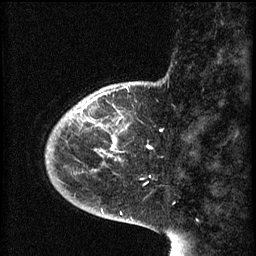
Breast MRI (dynamic contrast-enhanced), one sagittal slice; slice 12 of 60 in the series (ordered by position); 3 images stored at this slice position (order not interpretable as contrast timing); 1.5 T; TE 4.2 ms, TR 8.1 ms; 2 mm slice thickness; 256 × 256 image matrix, field of view 200 × 200 mm. Patient: female, 44 years.
Structures marked on this image (semi-automatic segmentation, software-assisted and operator-edited):
- analysis volume of interest (the breast-tissue region the enhancement analysis was run in; not a lesion): box from (x=59, y=110) to (x=128, y=165) px
- tumour enhancement mask (voxels above the 70 % enhancement threshold inside the analysis volume of interest): (x=69, y=110)–(x=118, y=157)